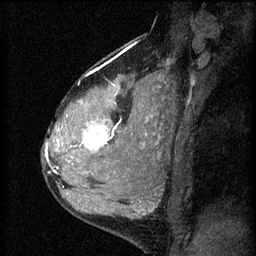
Breast MRI (dynamic contrast-enhanced), one sagittal slice. Slice 41 of 60 in the series (ordered by position). 3 images stored at this slice position (order not interpretable as contrast timing). 1.5 T. TE 4.2 ms, TR 8.2 ms. 2 mm slice thickness. 256 × 256 image matrix. Female patient, age 37 years.
Outlined on this slice (semi-automatic segmentation, software-assisted and operator-edited):
- analysis volume of interest (the breast-tissue region the enhancement analysis was run in; not a lesion): bounding box [x1, y1, x2, y2] px = [53, 78, 140, 181]
- tumour enhancement mask (voxels above the 70 % enhancement threshold inside the analysis volume of interest): [57, 122, 116, 173]